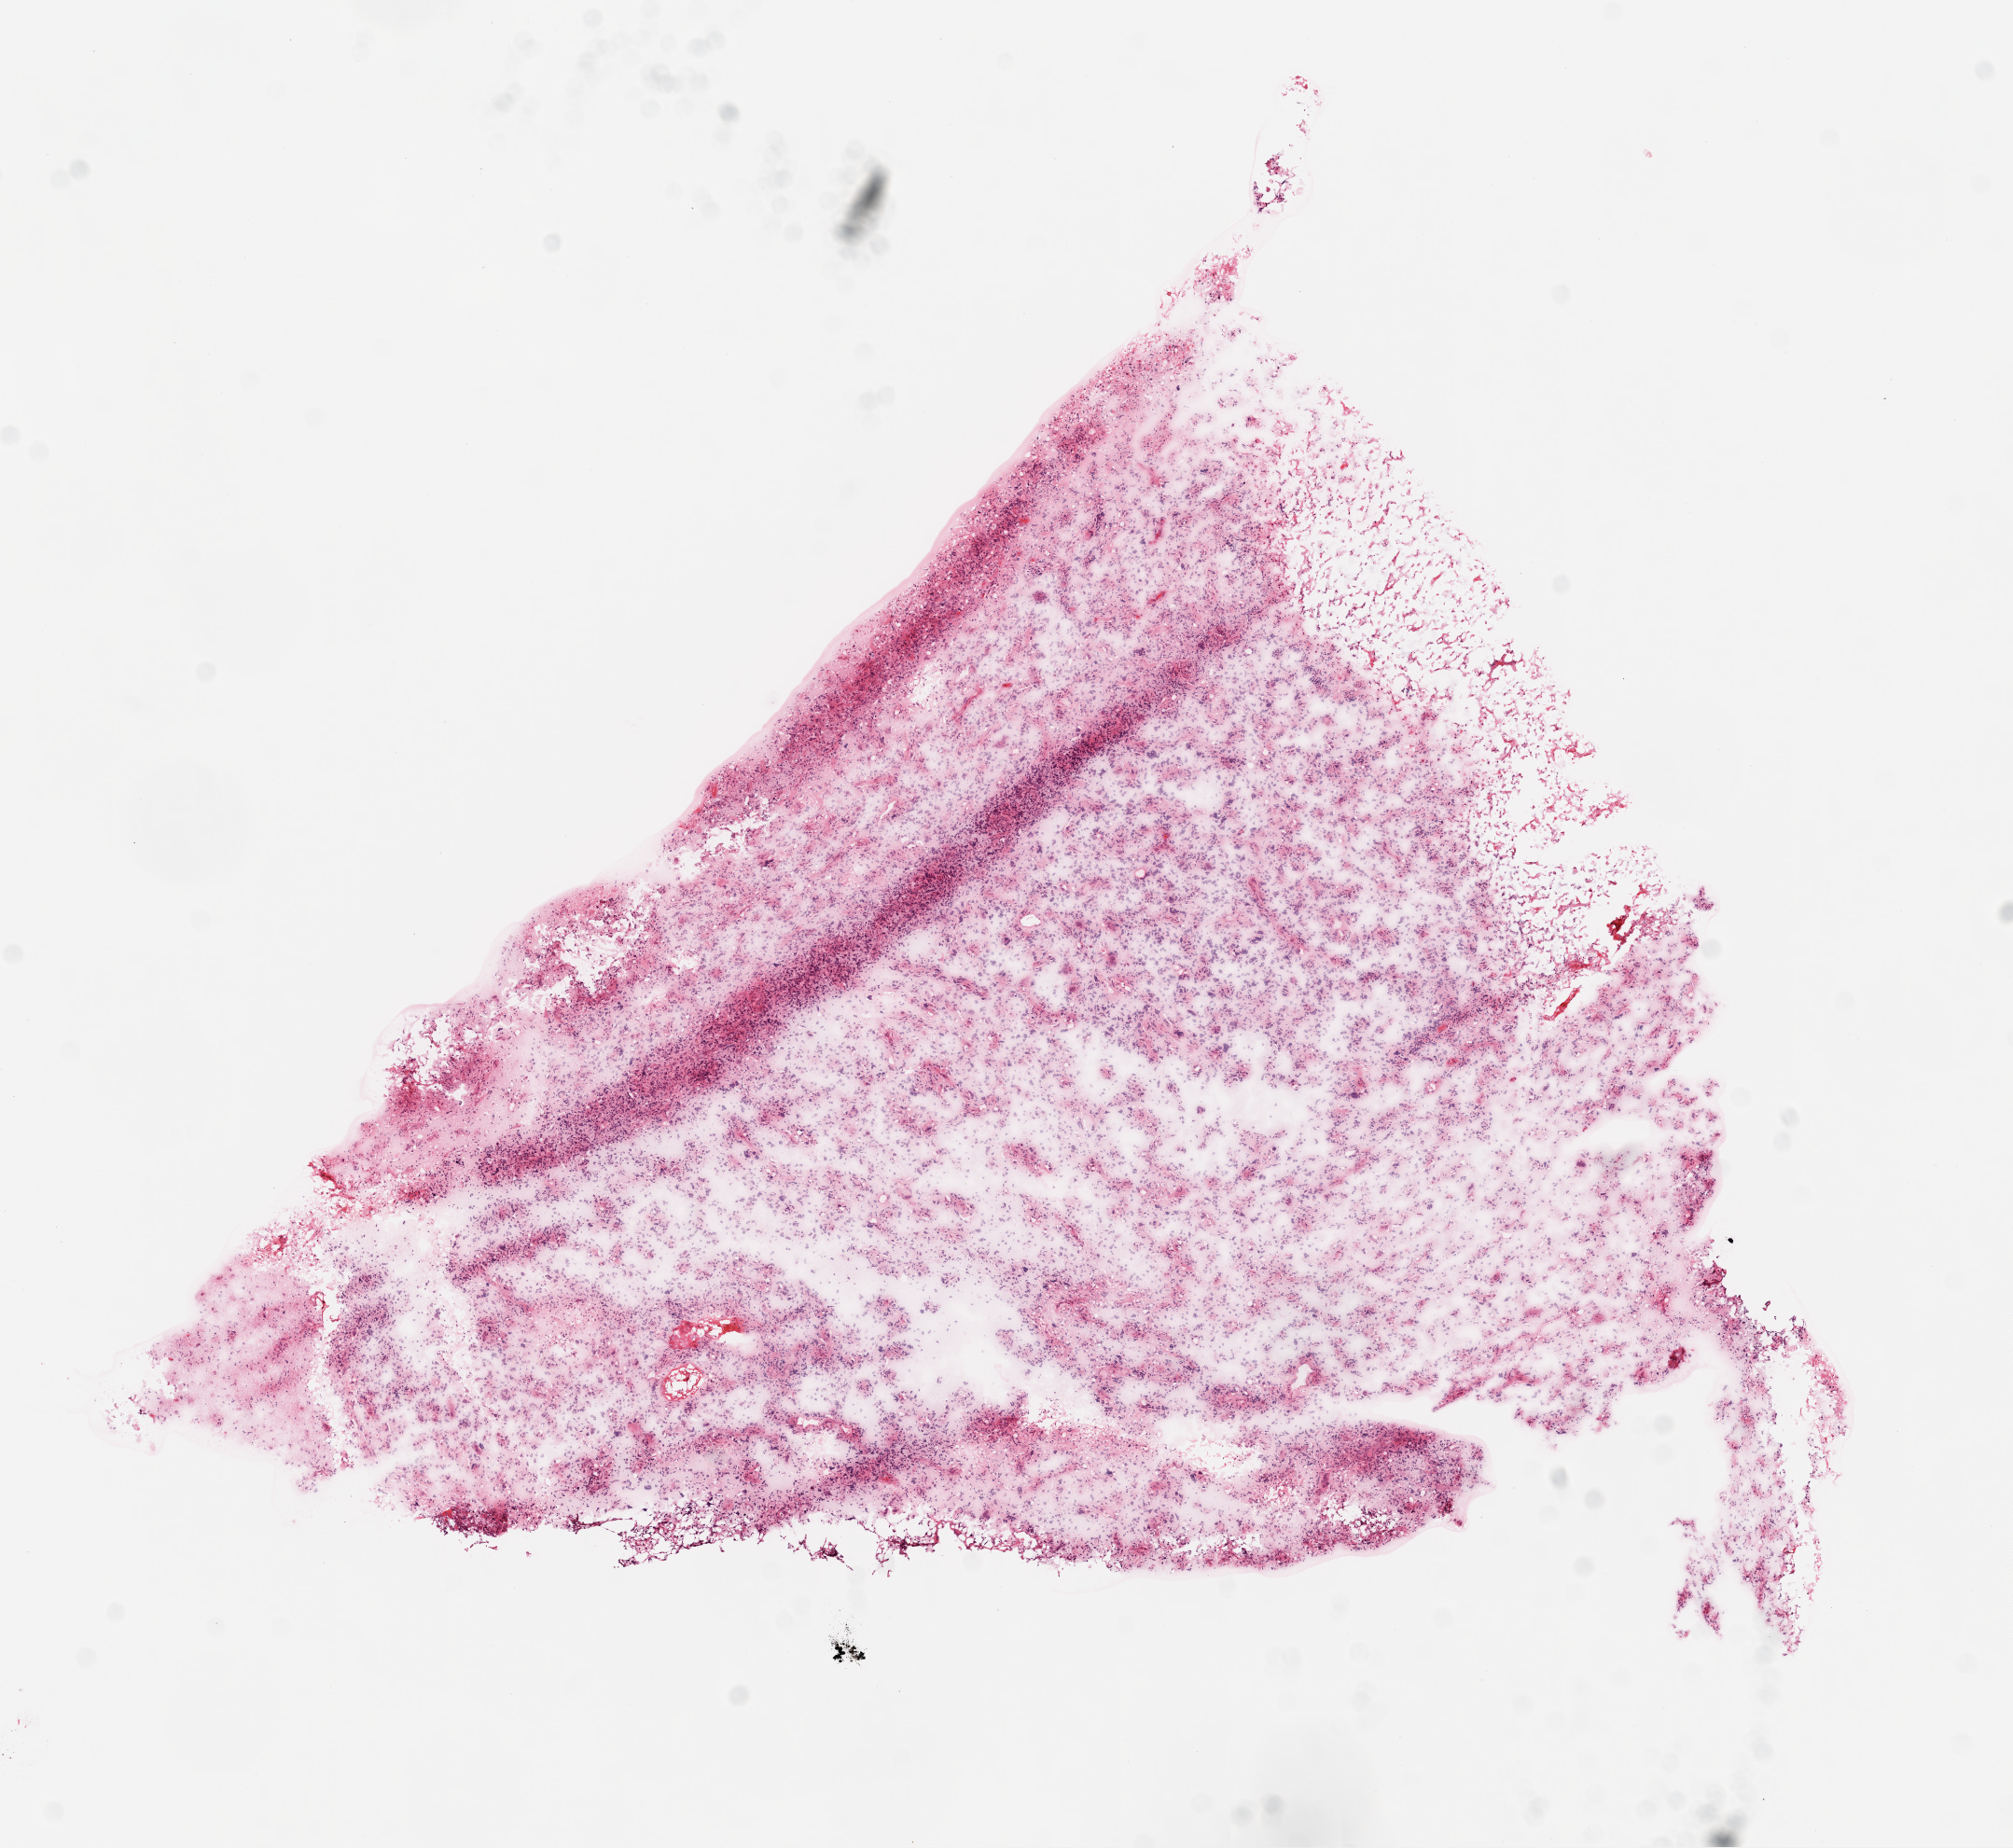
Hematoxylin and eosin (H&E) stained whole-slide image, low-resolution overview of the scanned area, about 8.7 x 8.0 mm (from a 20x scan); frozen section from the bottom of the tissue portion; primary tumour sample from the brain. Male patient; age at initial diagnosis 32 years. Composition of this section per pathologist review: tumour cells 95%, tumour nuclei 95%.
Histologic diagnosis: Glioblastoma.